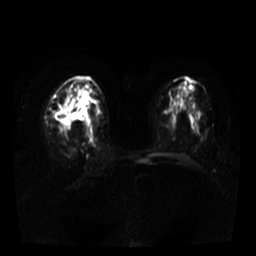
Breast MRI, one axial slice. Diffusion-weighted series; image 2 of 4 stored at this slice position (different b-values; order by instance number). 3 T. 5 mm slice thickness. 256 × 256 image matrix, field of view 320 × 320 mm. Female patient.
Structures marked on this image (outlined manually by an expert reader):
- tumour on diffusion-weighted imaging: bounding box (x1, y1, x2, y2) in pixels: (60, 105, 75, 134)